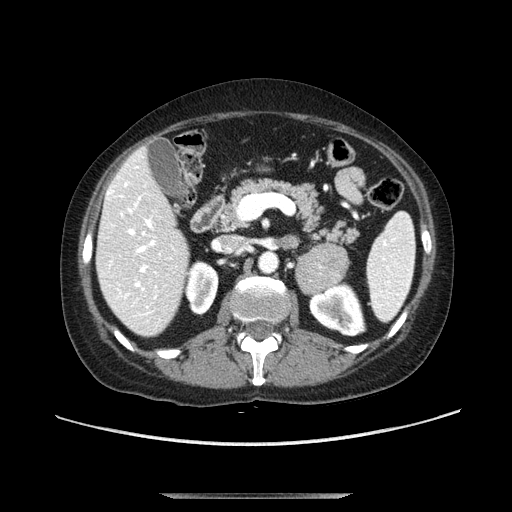
Contrast-enhanced abdominal CT, one axial slice; position 57 of 107 along the scan axis; soft-tissue window (W 400 / L 40 HU); 2.5 mm slice thickness; 512 × 512 image matrix. Female patient. Case-level facts recorded for this patient, not image findings: diagnosis: adrenocortical carcinoma; tumour side: left adrenal.
Annotated regions visible in this slice (semi-automatically segmented with operator editing):
- mass: bounding box (x1, y1, x2, y2) in pixels: (296, 242, 349, 294)